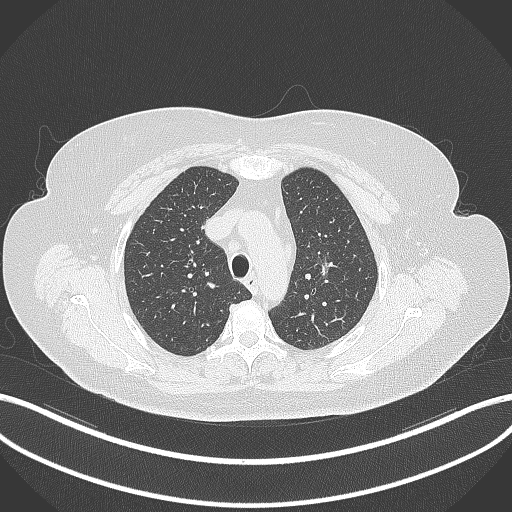
Chest CT, one axial slice; slice 257 of 309 in the series (ordered by position); 120 kVp; lung window (W 1500 / L -600 HU); 1 mm slice thickness; 512 × 512 image matrix. Female patient, age 70 years. From the clinical record (not read from this slice): clinical TNM (as recorded): T1c N0 M0.
Outlined on this slice (rectangle marked by the reading radiologist):
- lung tumour (recorded histology: adenocarcinoma): bounding box <317,257,337,282> (left, top, right, bottom; pixels)